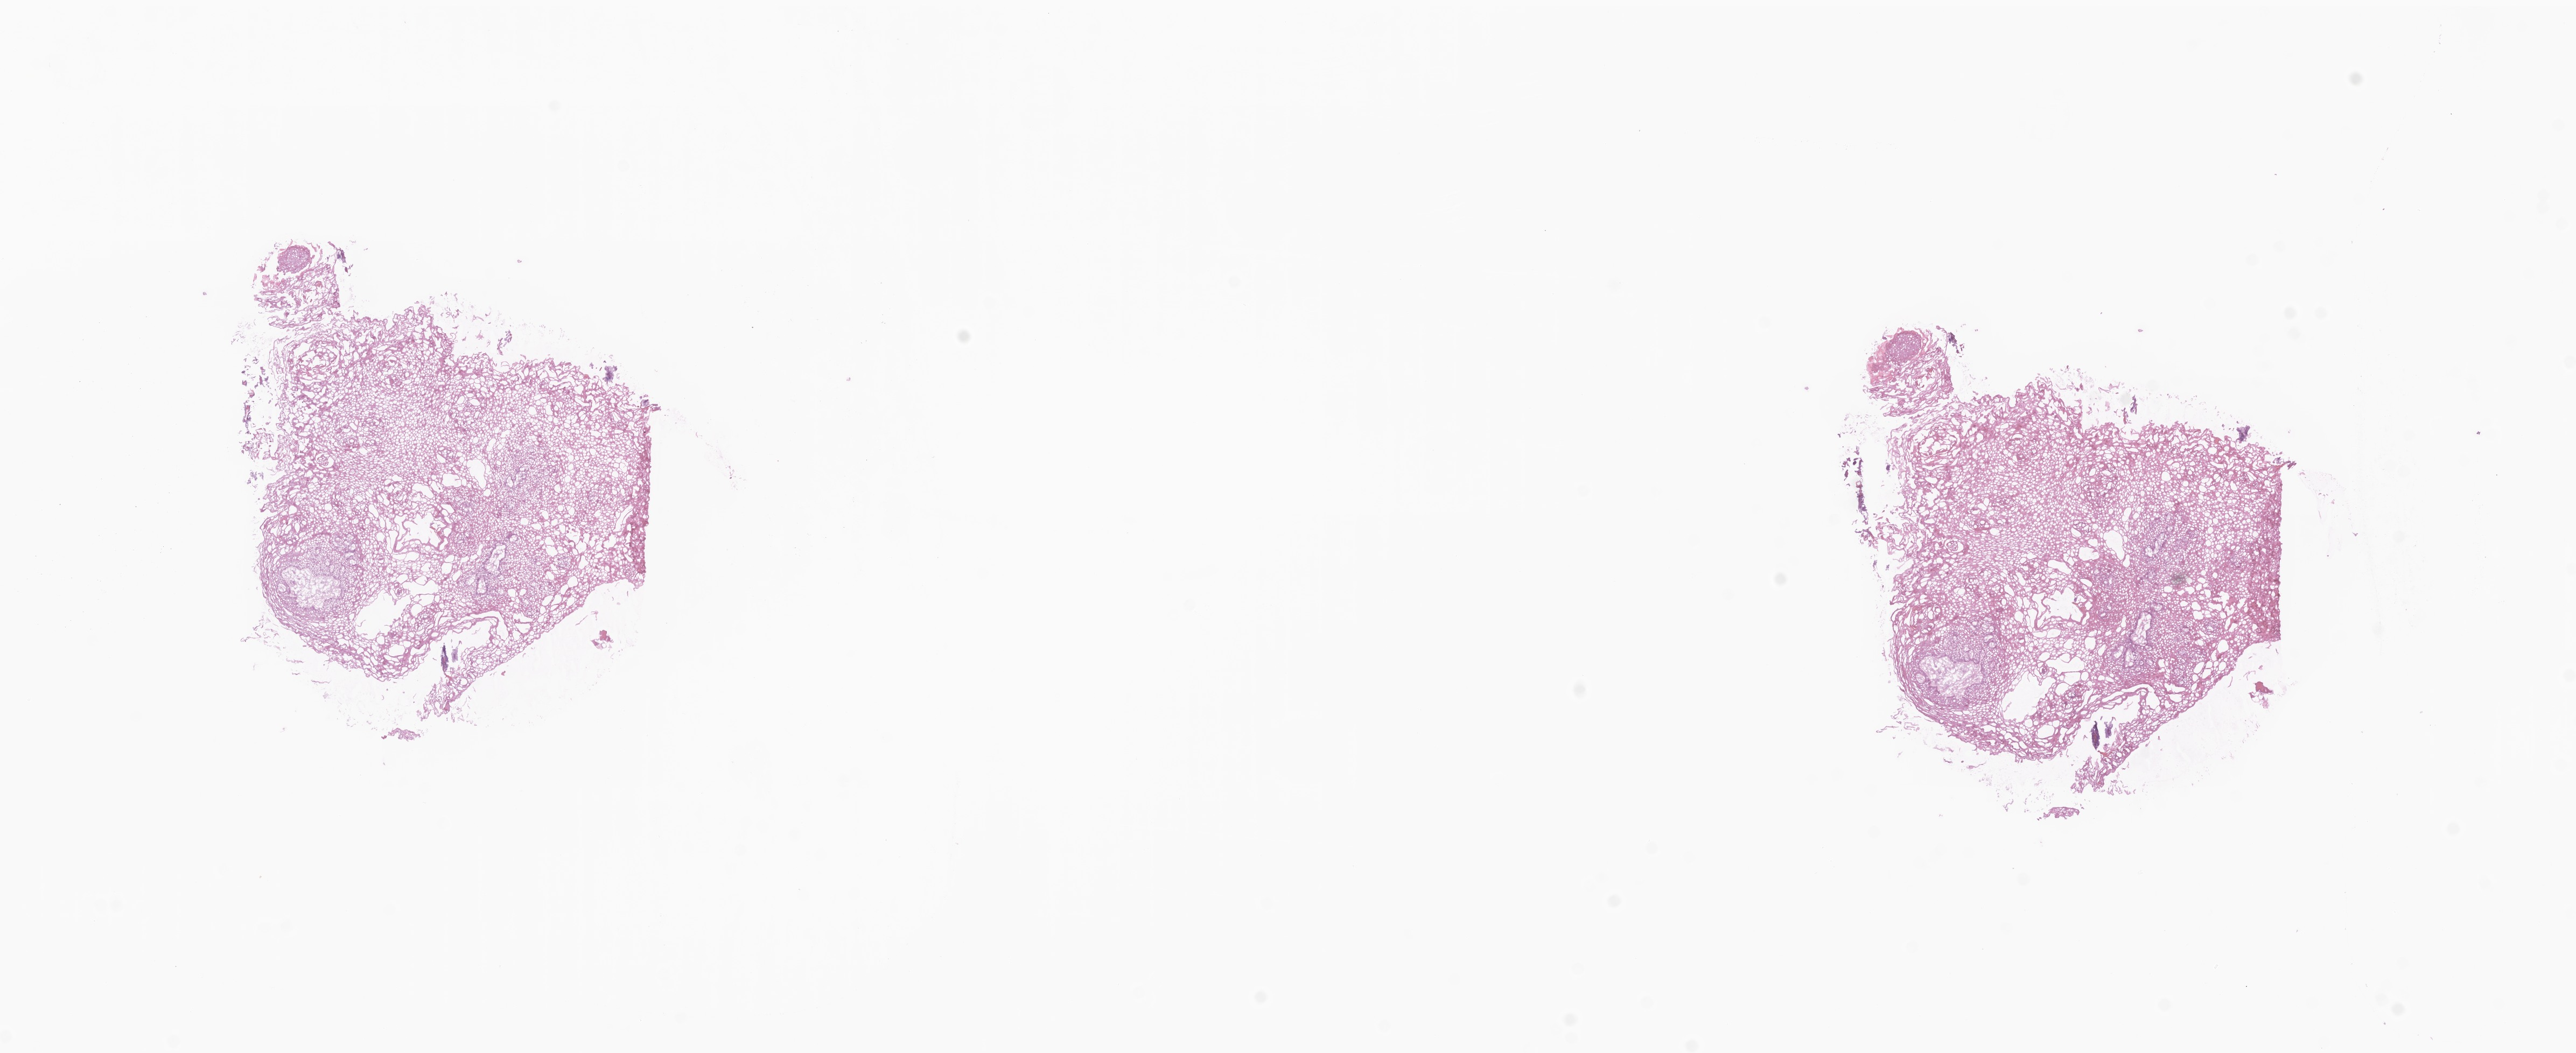
Digitized hematoxylin and eosin (H&E)-stained section — low-resolution overview of the scanned area, about 20.2 x 8.2 mm; cryosection; specimen: non-tumor (normal tissue) sample from a patient with squamous cell carcinoma, NOS; anatomic site: tongue (right). Patient sex: female. Slide review estimates, as recorded: tumor cells 0%, tumor nuclei 0%, stromal cells 100%, necrosis 0%, normal cells 0%. Inflammatory infiltration, as recorded: lymphocyte infiltration 0%, monocyte infiltration 0%, neutrophil infiltration 0%.
* this section: non-tumor tissue sample; the patient's diagnosis is given above